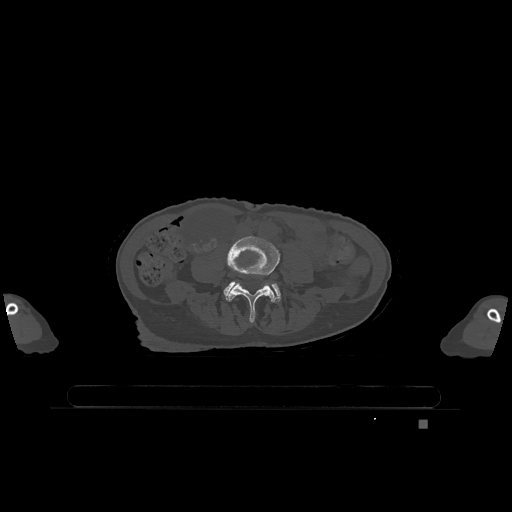
CT including the spine, one axial slice; position 285 of 1317 along the scan axis; bone window (W 1800 / L 400 HU); 0.5 mm slice thickness; 512 × 512 image matrix, field of view 500 × 500 mm. Female patient, age 74 years. From the clinical record (not read from this slice): primary cancer: lung; vertebrae with lytic lesions (as recorded): T1, T4, T5, T6, L4, L5.
Outlined on this slice (semi-automatically segmented with operator editing):
- L4 vertebra: bounding box [x1, y1, x2, y2] px = [226, 235, 280, 322]
- L5 vertebra: [224, 281, 281, 302]